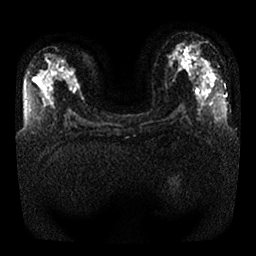
Breast MRI, one axial slice. Slice 13 of 32 in the series (ordered by position). Diffusion-weighted series; image 2 of 4 stored at this slice position (different b-values; order by instance number). 1.5 T. 4 mm slice thickness. 256 × 256 image matrix, field of view 350 × 350 mm. Female patient.
Annotated regions visible in this slice (manually delineated by an expert):
- tumour on diffusion-weighted imaging: bounding box [x1, y1, x2, y2] px = [70, 80, 81, 90]